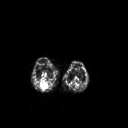
FDG PET of an extremity soft-tissue mass (from a PET/CT study), one axial slice. Slice 163 of 267 in the series (ordered by position). 3.27 mm slice thickness. 128 × 128 image matrix, field of view 500 × 500 mm. Female patient, age 62 years. From the clinical record (not read from this slice): histological type: liposarcoma; site of the primary tumour: right thigh.
Outlined on this slice (expert contour drawn on MRI and transferred to this co-registered scan by the dataset authors):
- gross tumour volume (mass): box from (x=42, y=84) to (x=48, y=89) px